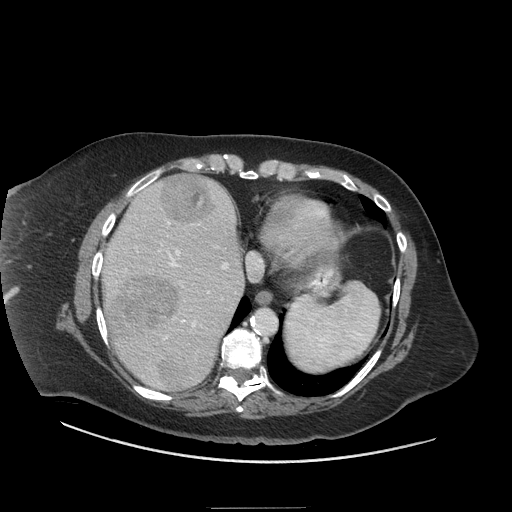
Contrast-enhanced abdominal CT (liver protocol), one axial slice. Slice 55 of 81 in the series (ordered by position). Reconstruction kernel STANDARD. 140 kVp. Soft-tissue window (W 400 / L 40 HU). 512 × 512 image matrix, field of view 440 × 440 mm. From the clinical record (not read from this slice): diagnosis: hepatocellular carcinoma (patient treated with transarterial chemoembolisation; whether this scan precedes or follows treatment is not stated here); TNM stage (as recorded): Stage-II; Child-Pugh class: A; tumour differentiation: moderately differentiated; tumour nodularity: multinodular.
Outlined on this slice (semi-automatic segmentation, software-assisted and operator-edited):
- liver parenchyma outside the tumour (the mass and vessels are separate outlines, so this box may not span the whole liver): bounding box <102,178,244,390> (left, top, right, bottom; pixels)
- mass: <115,171,215,390>
- liver vessels: <108,221,228,385>